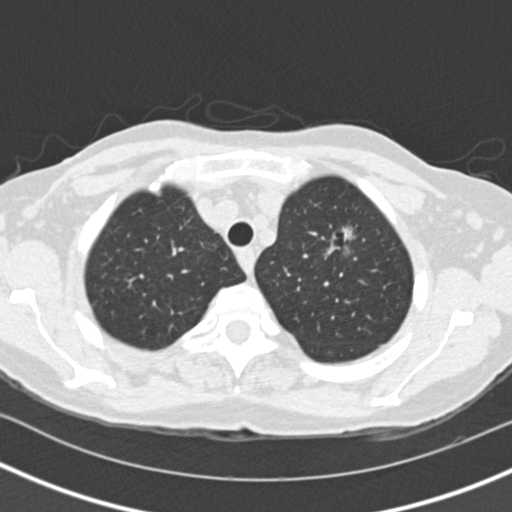
Low-dose screening chest CT, one axial slice. Slice 121 of 146 in the series (ordered by position). Lung window (W 1500 / L -600 HU). 2 mm slice thickness. 512 × 512 image matrix, field of view 310 × 310 mm.
Outlined on this slice (manually delineated by an expert):
- lesion 1 (tumor, upper lobe of left lung): bounding box (x1, y1, x2, y2) in pixels: (342, 227, 353, 240)